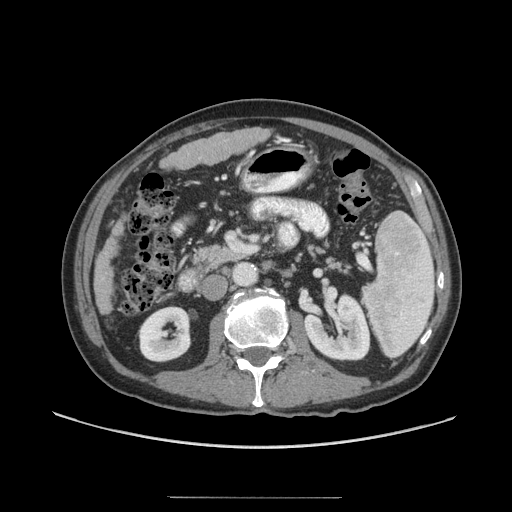
Contrast-enhanced abdominal CT (liver protocol), one axial slice; position 15 of 71 along the scan axis; reconstruction kernel STANDARD; 140 kVp; soft-tissue window (W 400 / L 40 HU); 2.5 mm slice thickness; 512 × 512 image matrix, field of view 400 × 400 mm. Case-level facts recorded for this patient, not image findings: diagnosis: hepatocellular carcinoma (patient treated with transarterial chemoembolisation; whether this scan precedes or follows treatment is not stated here); TNM stage (as recorded): Stage-I; Child-Pugh class: A; tumour differentiation: well differentiated.
Annotated regions visible in this slice (semi-automatically segmented with operator editing):
- liver parenchyma outside the tumour (the mass and vessels are separate outlines, so this box may not span the whole liver): bounding box (x1, y1, x2, y2) in pixels: (94, 126, 270, 314)